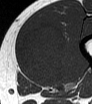
MRI of an extremity soft-tissue mass, one axial slice; slice 23 of 62 in the series (ordered by position); MR volume resampled by the dataset authors to the PET/CT grid (not the native acquisition matrix); 3.27 mm slice thickness; 92 × 104 image matrix, field of view 90 × 102 mm. Male patient. From the clinical record (not read from this slice): histological type: mixoid liposarcoma; grade: low; site of the primary tumour: left thigh.
Outlined on this slice (expert contour drawn on MRI and transferred to this co-registered scan by the dataset authors):
- gross tumour volume (mass): bounding box [x1, y1, x2, y2] px = [19, 22, 68, 84]